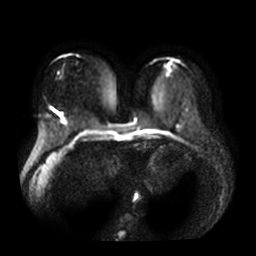
Breast MRI, one axial slice; slice 14 of 36 in the series (ordered by position); diffusion-weighted series; image 2 of 4 stored at this slice position (different b-values; order by instance number); 3 T; 256 × 256 image matrix, field of view 360 × 360 mm. Female patient.
Annotated regions visible in this slice (expert manual segmentation):
- tumour on diffusion-weighted imaging: bounding box <61,118,67,123> (left, top, right, bottom; pixels)